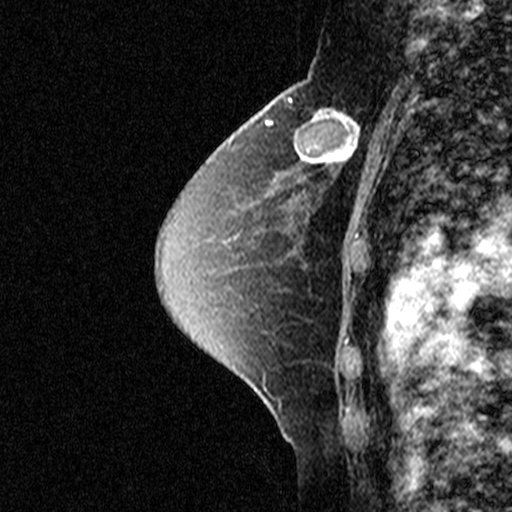
Breast MRI (dynamic contrast-enhanced), one sagittal slice. Position 27 of 44 along the scan axis. Dynamic contrast-enhanced study with each time point stored as its own series, time point 2 of 3 at this slice position (early post-contrast, ordered by acquisition time). 1.5 T. TE 4.5 ms, TR 11 ms. 3 mm slice thickness. 512 × 512 image matrix, field of view 200 × 200 mm. Female patient, age 49 years. Case-level facts recorded for this patient, not image findings: setting: breast cancer imaged before/during neoadjuvant chemotherapy; receptor status: triple-negative.
Structures marked on this image (semi-automatic segmentation, software-assisted and operator-edited):
- analysis volume of interest (the breast-tissue region the enhancement analysis was run in; not a lesion): bounding box (x1, y1, x2, y2) in pixels: (276, 94, 369, 181)
- tumour enhancement mask (voxels above the 90 % enhancement threshold inside the analysis volume of interest): (312, 109, 360, 165)